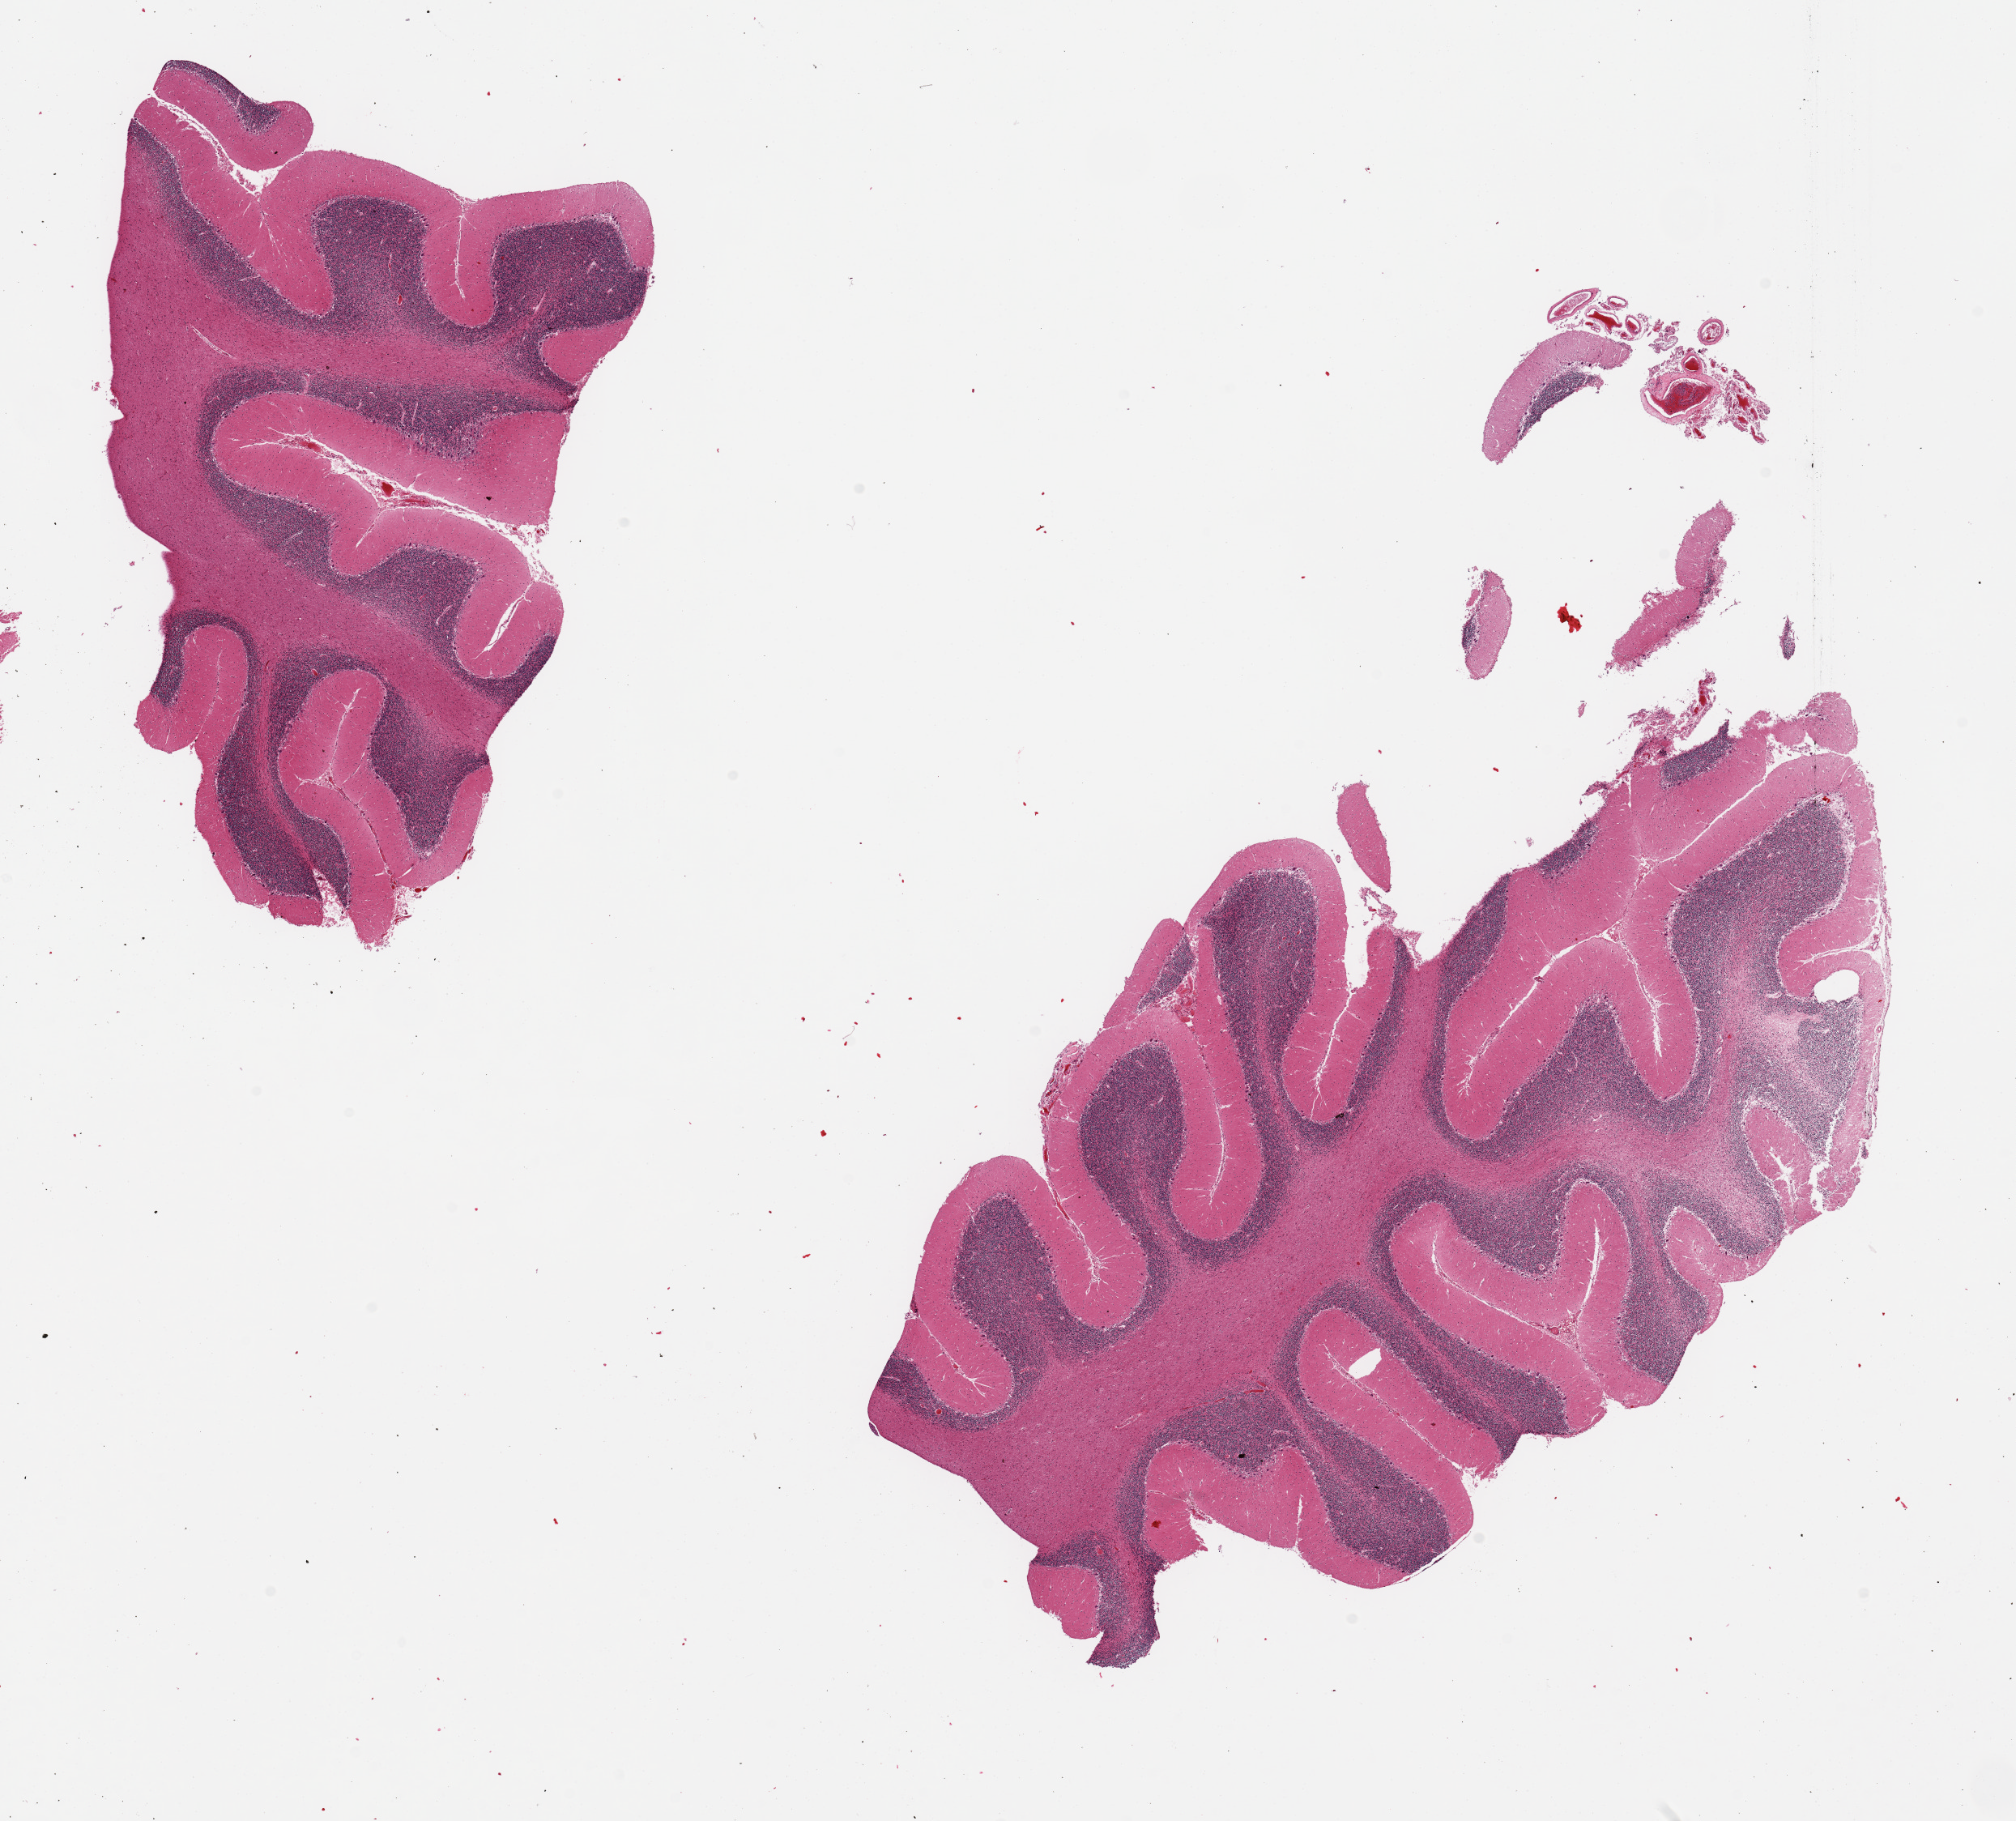
Hematoxylin and eosin (H&E) whole-slide image — low-resolution overview of the scanned area, about 19.7 x 17.8 mm; PAXgene-fixed paraffin-embedded (PFPE) section; section of cerebellum (target tissue); tissue donor sample. Donor sex: female.
Pathologist's review note for this sample: 2 pieces; Purkinje cells present.